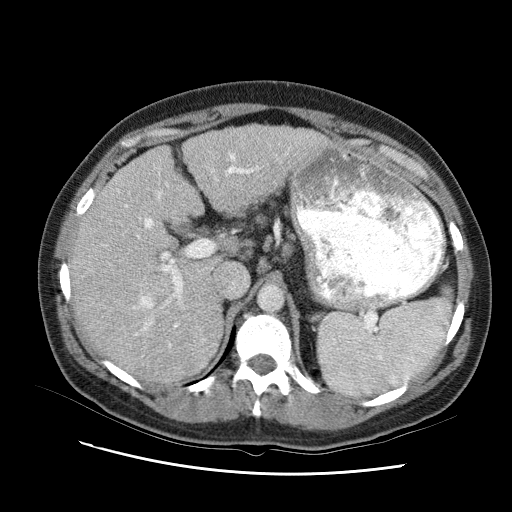
Contrast-enhanced abdominal CT (liver protocol), one axial slice. Position 62 of 95 along the scan axis. Reconstruction kernel STANDARD. One of 2 acquisitions stored at this slice position. Soft-tissue window (W 400 / L 40 HU). 2.5 mm slice thickness. 512 × 512 image matrix, field of view 360 × 360 mm. Case-level facts recorded for this patient, not image findings: diagnosis: hepatocellular carcinoma (patient treated with transarterial chemoembolisation; whether this scan precedes or follows treatment is not stated here); TNM stage (as recorded): Stage-I; Child-Pugh class: B; tumour differentiation: moderately differentiated.
Annotated regions visible in this slice (semi-automatic segmentation, software-assisted and operator-edited):
- abdominal aorta: bounding box <258,284,283,310> (left, top, right, bottom; pixels)
- liver parenchyma outside the tumour (the mass and vessels are separate outlines, so this box may not span the whole liver): <68,120,335,374>
- liver vessels: <104,146,291,356>